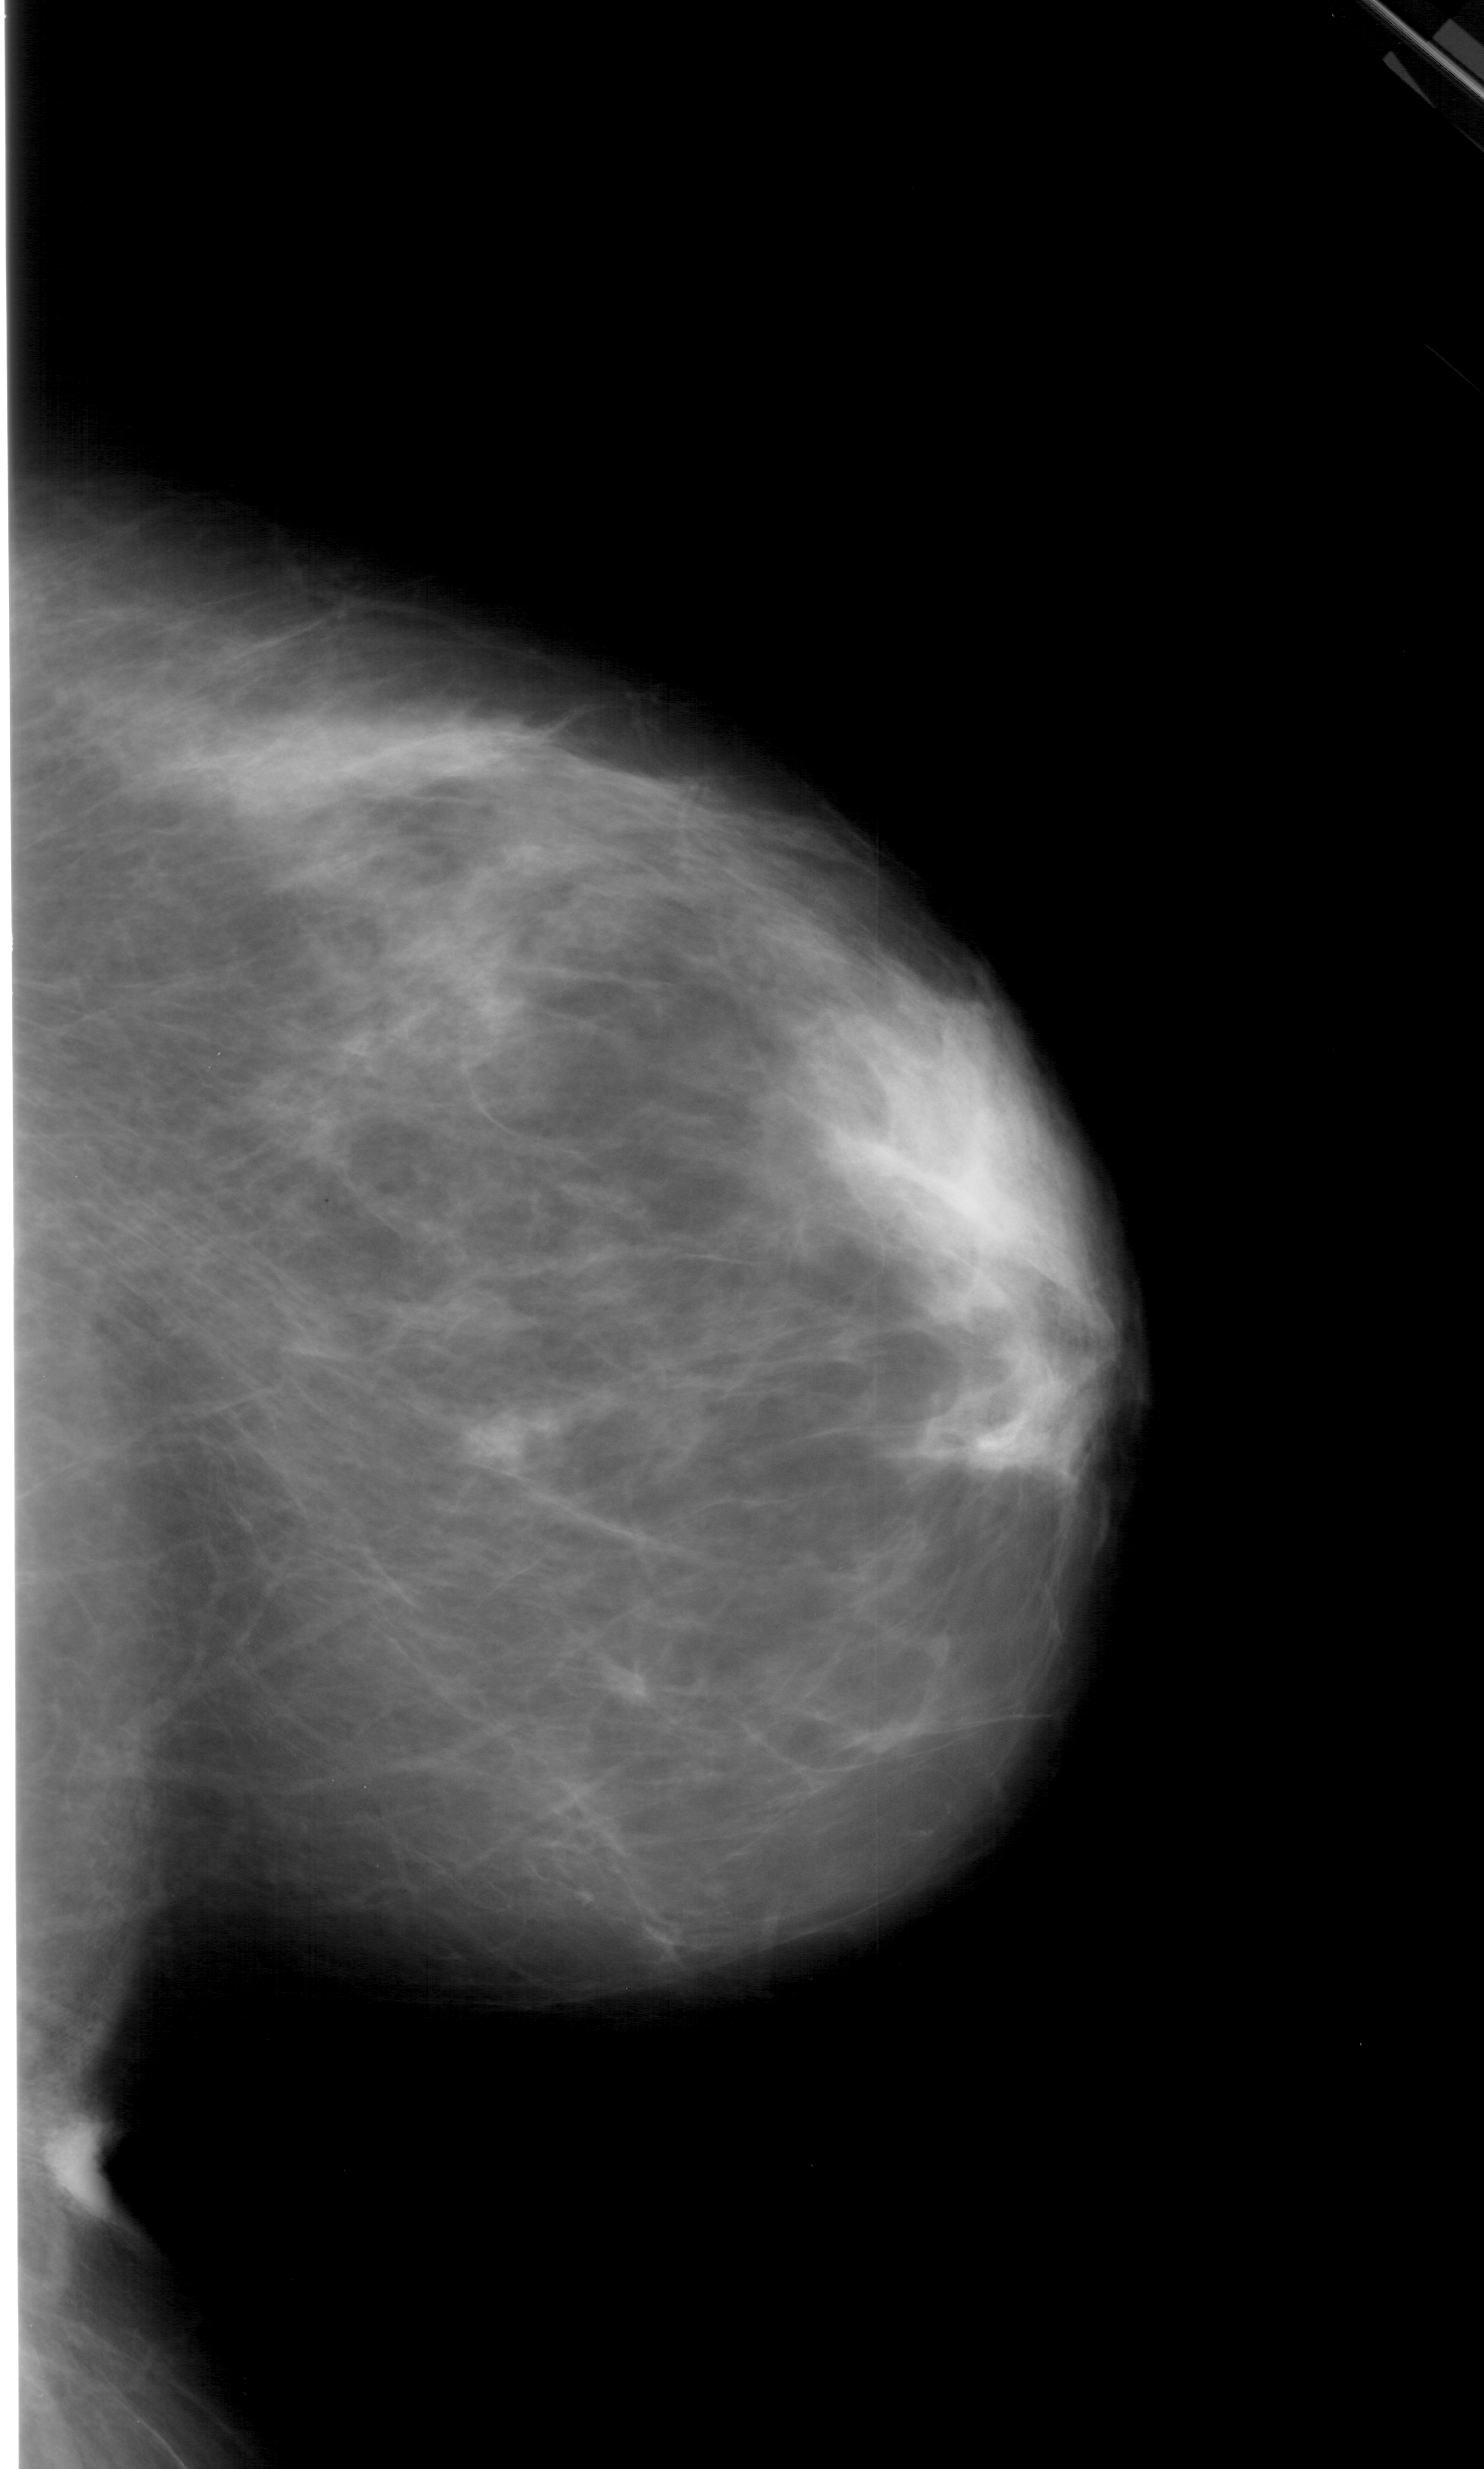
Digitized screen-film mammogram. Right breast. CC view. Breast composition: heterogeneously dense (BI-RADS density category 3 of 4). 1484 × 2469 image matrix.
Expert-marked regions of interest on this image (one box per marked abnormality):
- mass, shape oval, margins circumscribed; BI-RADS assessment category 4; pathology result (as recorded, not read from the image): benign: box from (x=444, y=1389) to (x=575, y=1510) px